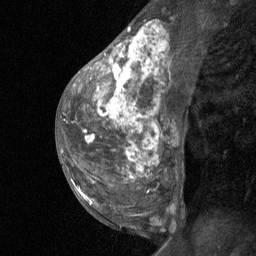
Breast MRI (dynamic contrast-enhanced), one sagittal slice; slice 34 of 64 in the series (ordered by position); dynamic contrast-enhanced study with each time point stored as its own series, time point 2 of 3 at this slice position (early post-contrast, ordered by acquisition time); 1.5 T; TE 4.8 ms, TR 27 ms; 2 mm slice thickness; 256 × 256 image matrix, field of view 180 × 180 mm. Patient: female, 36 years. From the clinical record (not read from this slice): setting: breast cancer imaged before/during neoadjuvant chemotherapy; receptor status: HR-positive, HER2-negative.
Structures marked on this image (semi-automatic segmentation, software-assisted and operator-edited):
- analysis volume of interest (the breast-tissue region the enhancement analysis was run in; not a lesion): bounding box [x1, y1, x2, y2] px = [67, 12, 169, 237]
- tumour enhancement mask (voxels above the 90 % enhancement threshold inside the analysis volume of interest): [84, 27, 150, 178]